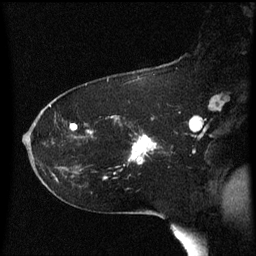
Breast MRI (dynamic contrast-enhanced), one sagittal slice; position 39 of 60 along the scan axis; dynamic contrast-enhanced series, image 2 of 3 at this slice position (ordered by acquisition); 1.5 T; TE 4.2 ms, TR 8.4 ms; 256 × 256 image matrix, field of view 200 × 200 mm. Female patient, age 54 years. Case-level facts recorded for this patient, not image findings: setting: breast cancer imaged before/during neoadjuvant chemotherapy; receptor status: HR-positive, HER2-negative.
Outlined on this slice (semi-automatically segmented with operator editing):
- analysis volume of interest (the breast-tissue region the enhancement analysis was run in; not a lesion): bounding box <117,124,158,169> (left, top, right, bottom; pixels)
- tumour enhancement mask (voxels above the 70 % enhancement threshold inside the analysis volume of interest): <130,136,157,163>